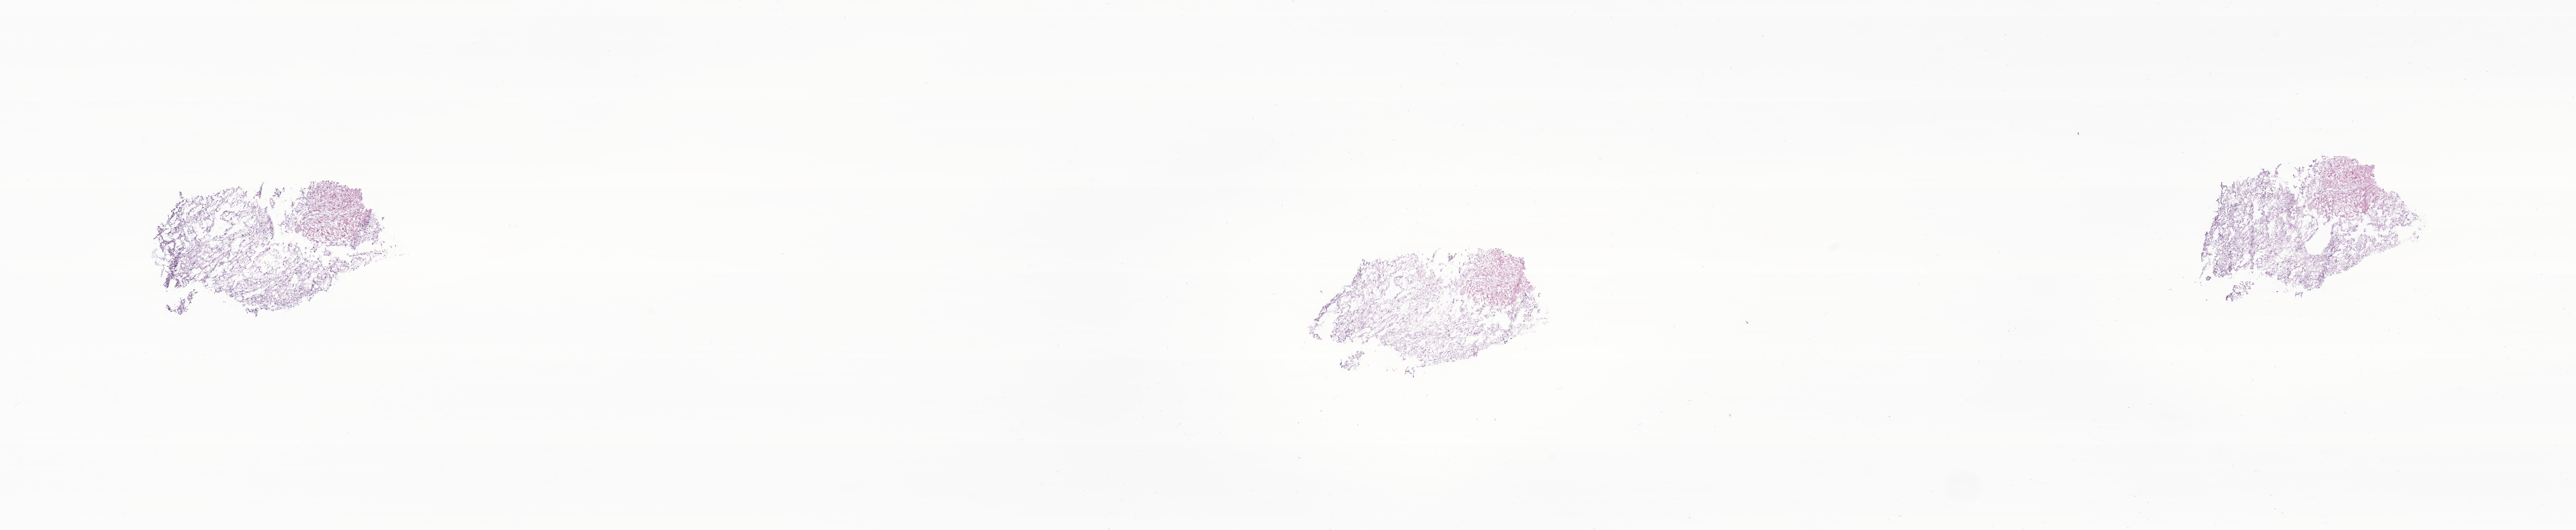
Whole-slide image, haematoxylin and eosin stain of tumor tissue from the cerebellum, whole scanned area (about 32.1 x 6.6 mm) shown as a low-resolution overview, frozen section. Female patient, age 146 months.
* diagnosis (ICD-O-3 morphology term): Pilocytic astrocytoma